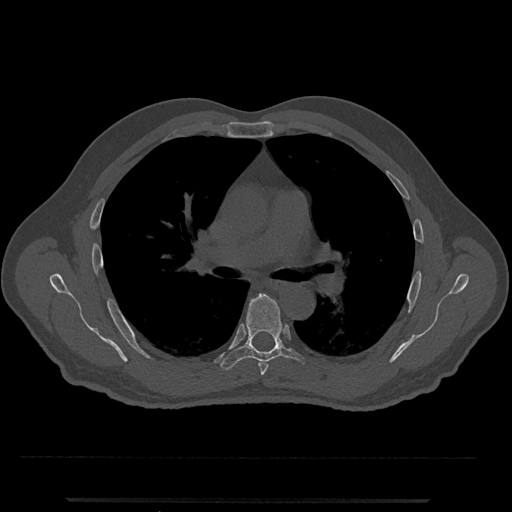
CT including the spine, one axial slice; slice 748 of 797 in the series (ordered by position); bone window (W 1800 / L 400 HU); 0.5 mm slice thickness; 512 × 512 image matrix, field of view 419 × 419 mm. Male patient, age 63 years. Case-level facts recorded for this patient, not image findings: primary cancer: prostate.
Outlined on this slice (semi-automatic segmentation, software-assisted and operator-edited):
- T5 vertebra: bounding box <259,362,268,375> (left, top, right, bottom; pixels)
- T6 vertebra: <220,294,306,371>